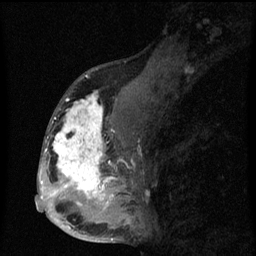
Breast MRI (dynamic contrast-enhanced), one sagittal slice. Slice 33 of 60 in the series (ordered by position). Dynamic contrast-enhanced series, image 2 of 3 at this slice position (ordered by acquisition). 1.5 T. TE 4.2 ms, TR 8 ms. 256 × 256 image matrix, field of view 190 × 190 mm. Female patient, age 50 years.
Structures marked on this image (semi-automatic segmentation, software-assisted and operator-edited):
- analysis volume of interest (the breast-tissue region the enhancement analysis was run in; not a lesion): bounding box <43,90,142,216> (left, top, right, bottom; pixels)
- tumour enhancement mask (voxels above the 70 % enhancement threshold inside the analysis volume of interest): <43,91,116,211>